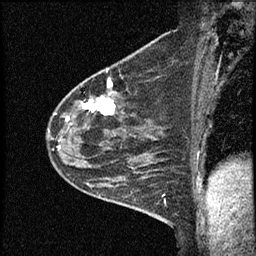
Breast MRI (dynamic contrast-enhanced), one sagittal slice. Slice 43 of 60 in the series (ordered by position). Dynamic contrast-enhanced study with each time point stored as its own series, time point 2 of 4 at this slice position (early post-contrast, ordered by acquisition time). 1.5 T. TE 4.2 ms, TR 17.6 ms. 256 × 256 image matrix, field of view 200 × 200 mm. Patient: female, 53 years. Case-level facts recorded for this patient, not image findings: setting: breast cancer imaged before/during neoadjuvant chemotherapy; receptor status: HR-positive, HER2-negative.
Outlined on this slice (semi-automatic segmentation, software-assisted and operator-edited):
- analysis volume of interest (the breast-tissue region the enhancement analysis was run in; not a lesion): box from (x=46, y=69) to (x=156, y=199) px
- tumour enhancement mask (voxels above the 100 % enhancement threshold inside the analysis volume of interest): (x=58, y=79)–(x=115, y=148)